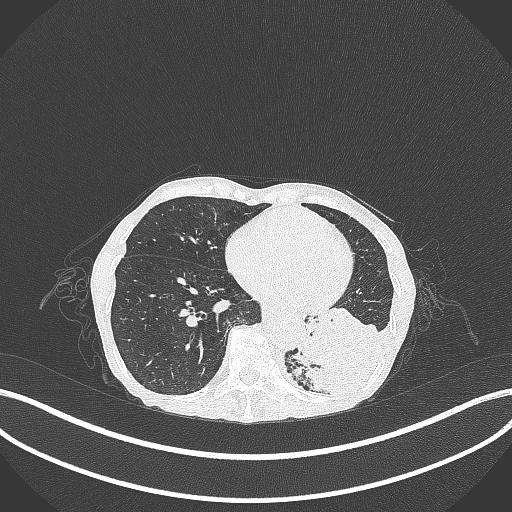
Chest CT, one axial slice. Slice 84 of 347 in the series (ordered by position). Reconstruction kernel B70f. Lung window (W 1500 / L -600 HU). 1 mm slice thickness. 512 × 512 image matrix, field of view 400 × 400 mm. Patient: female, 70 years. Case-level facts recorded for this patient, not image findings: clinical TNM (as recorded): T3 N0 M0; histopathological grade: G3.
Outlined on this slice (bounding box drawn by a radiologist):
- lung tumour (recorded histology: small cell carcinoma): bounding box (x1, y1, x2, y2) in pixels: (294, 319, 378, 407)